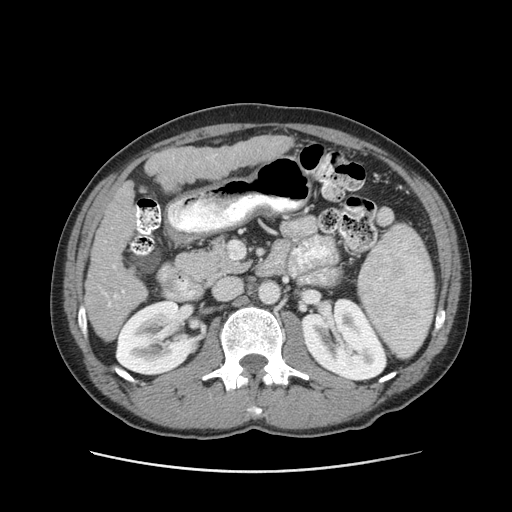
Contrast-enhanced abdominal CT (liver protocol), one axial slice; slice 38 of 93 in the series (ordered by position); soft-tissue window (W 400 / L 40 HU); 2.5 mm slice thickness; 512 × 512 image matrix, field of view 380 × 380 mm. Case-level facts recorded for this patient, not image findings: diagnosis: hepatocellular carcinoma (patient treated with transarterial chemoembolisation; whether this scan precedes or follows treatment is not stated here); TNM stage (as recorded): Stage-II; Child-Pugh class: A; tumour size: 1 cm.
Annotated regions visible in this slice (semi-automatic segmentation, software-assisted and operator-edited):
- liver parenchyma outside the tumour (the mass and vessels are separate outlines, so this box may not span the whole liver): bounding box (x1, y1, x2, y2) in pixels: (84, 136, 294, 342)
- liver vessels: (103, 266, 125, 307)